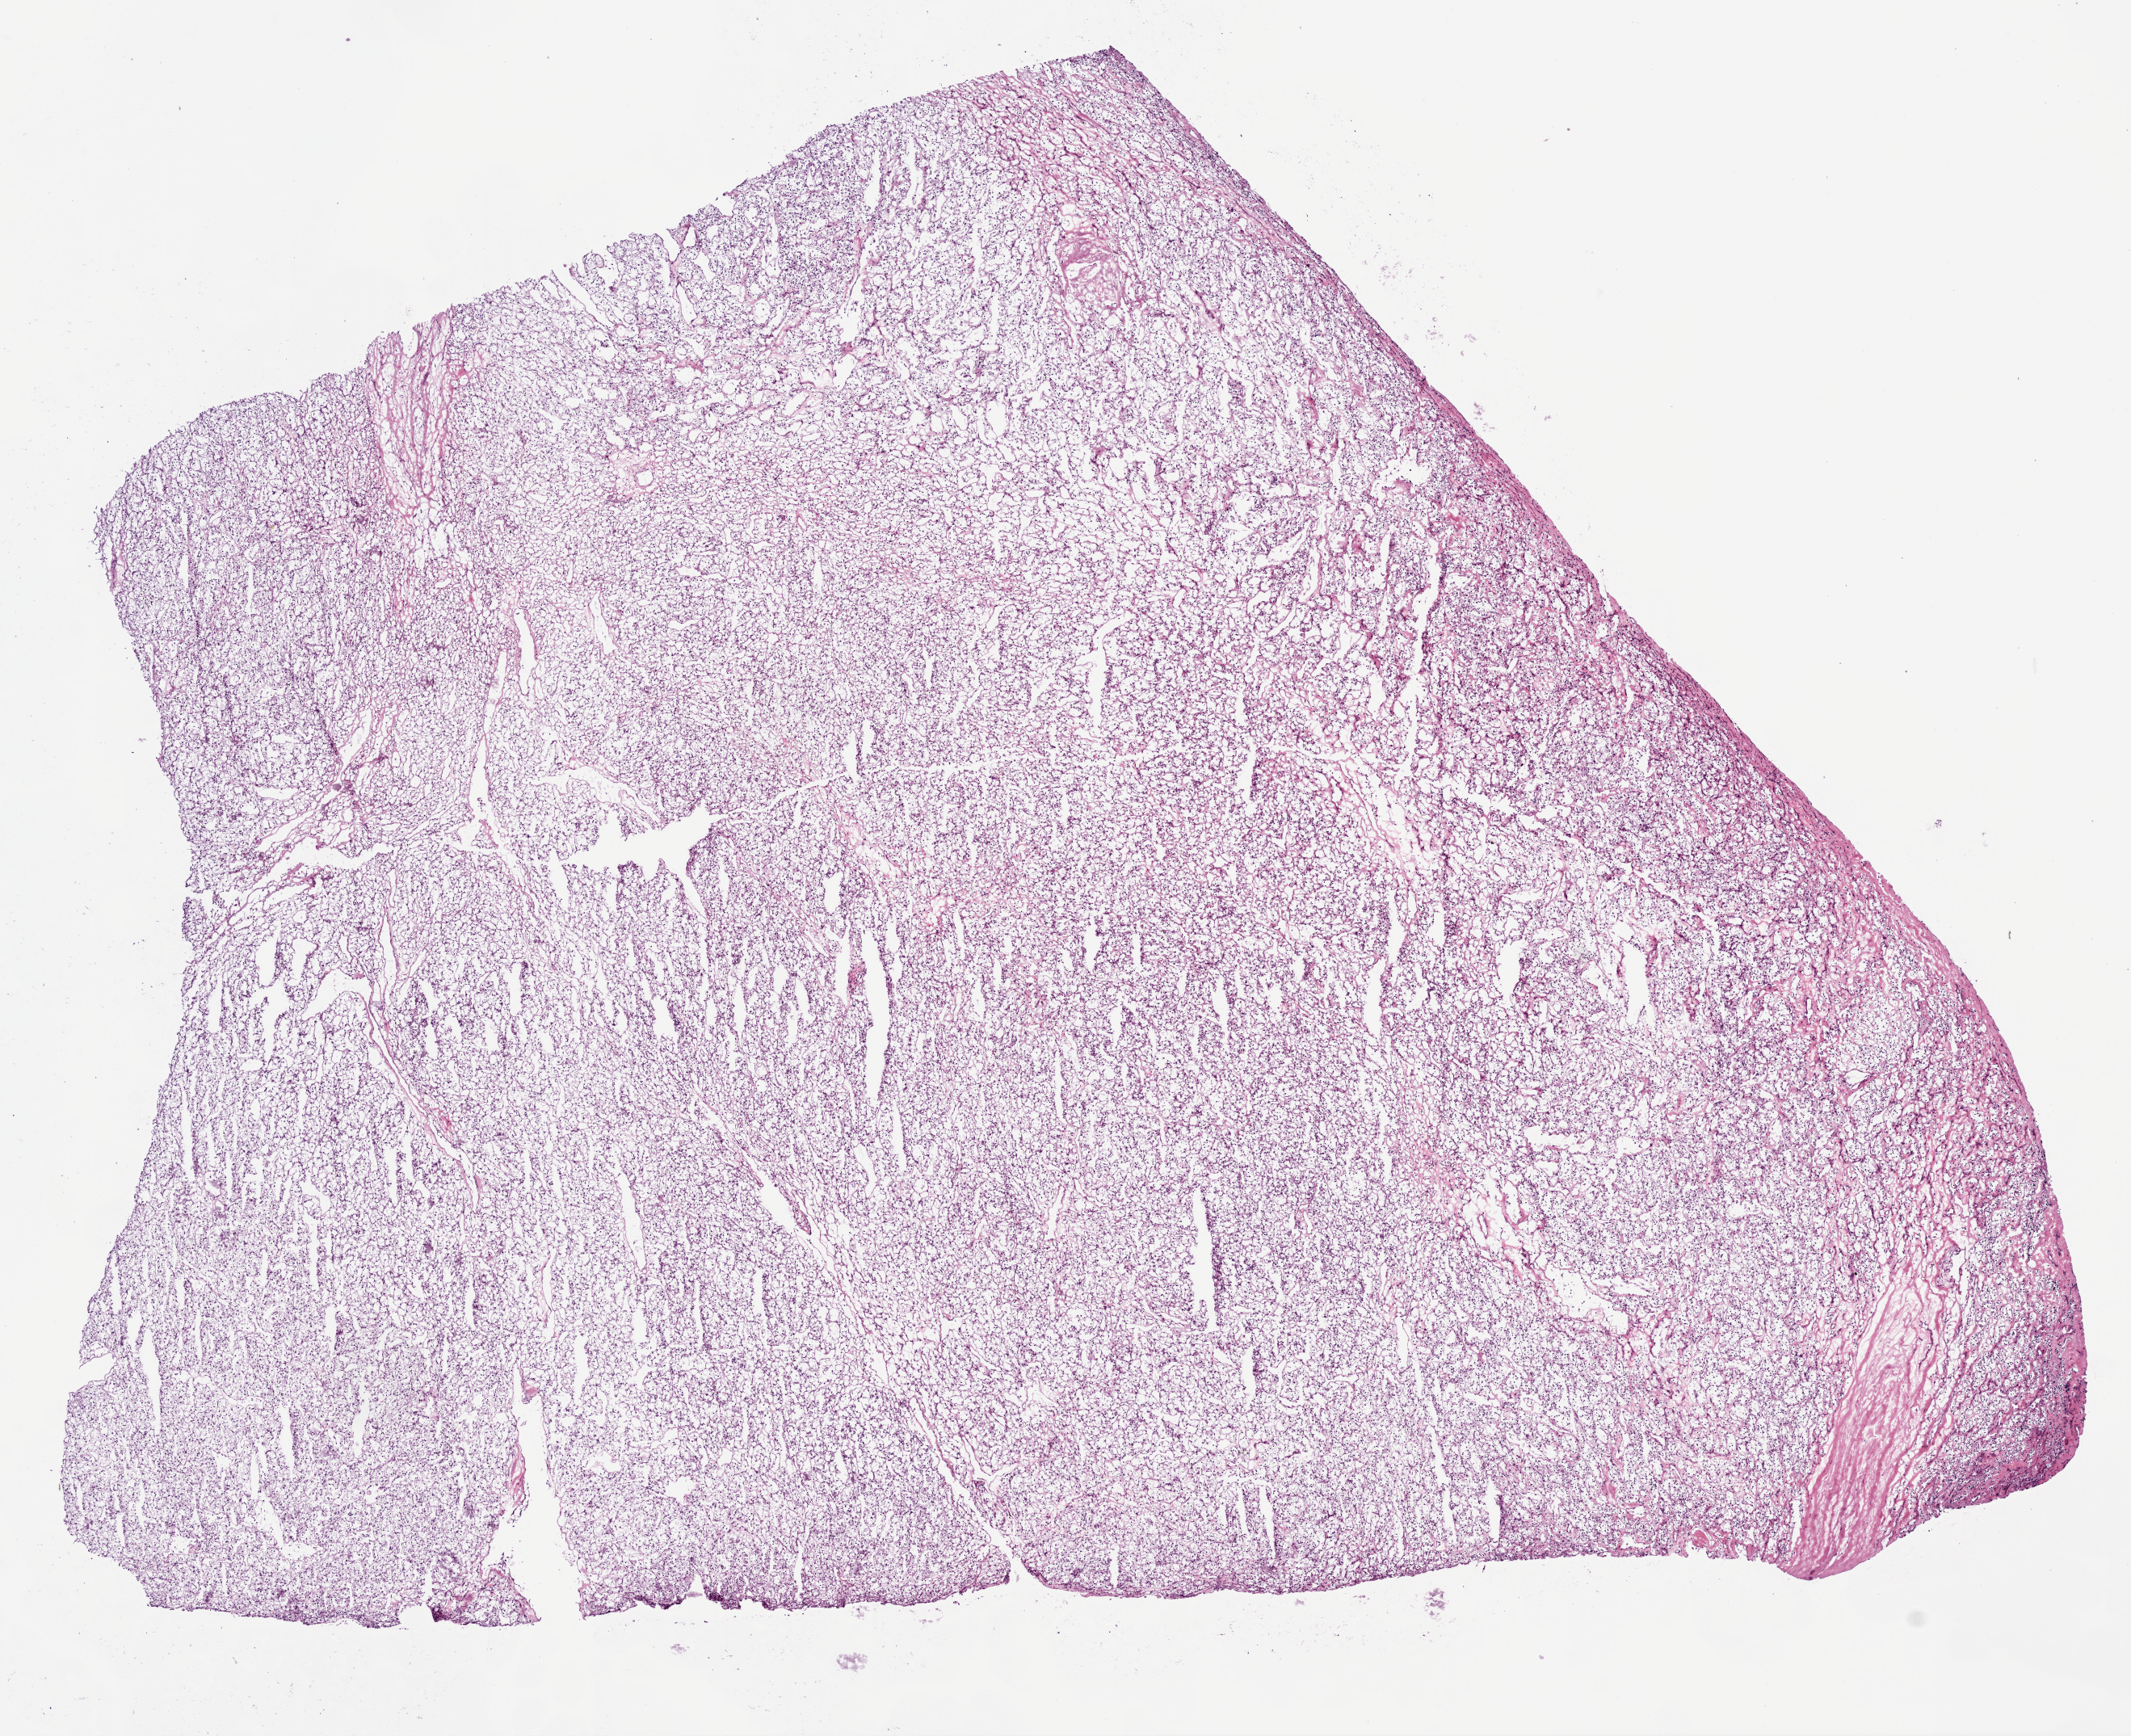
Whole-slide histology image, H&E, whole scanned area (about 10.6 x 8.7 mm) shown as a low-resolution overview; frozen section from the bottom of the tissue portion; sample: primary tumour, kidney. Female, age 61 years at initial diagnosis. Histologic grade: G1 (well differentiated). Pathologist review of this section (percent, as recorded): tumour cells 95%, tumour nuclei 90%, normal cells 0%, stromal cells 5%, necrosis 0%. Infiltration values recorded for this section: lymphocyte infiltration 0%, monocyte infiltration 0%, neutrophil infiltration 0%.
* histologic diagnosis: Clear cell adenocarcinoma, NOS
* AJCC pathologic stage: II (7th edition)
* TNM: T2 N0 M0
* laterality: right